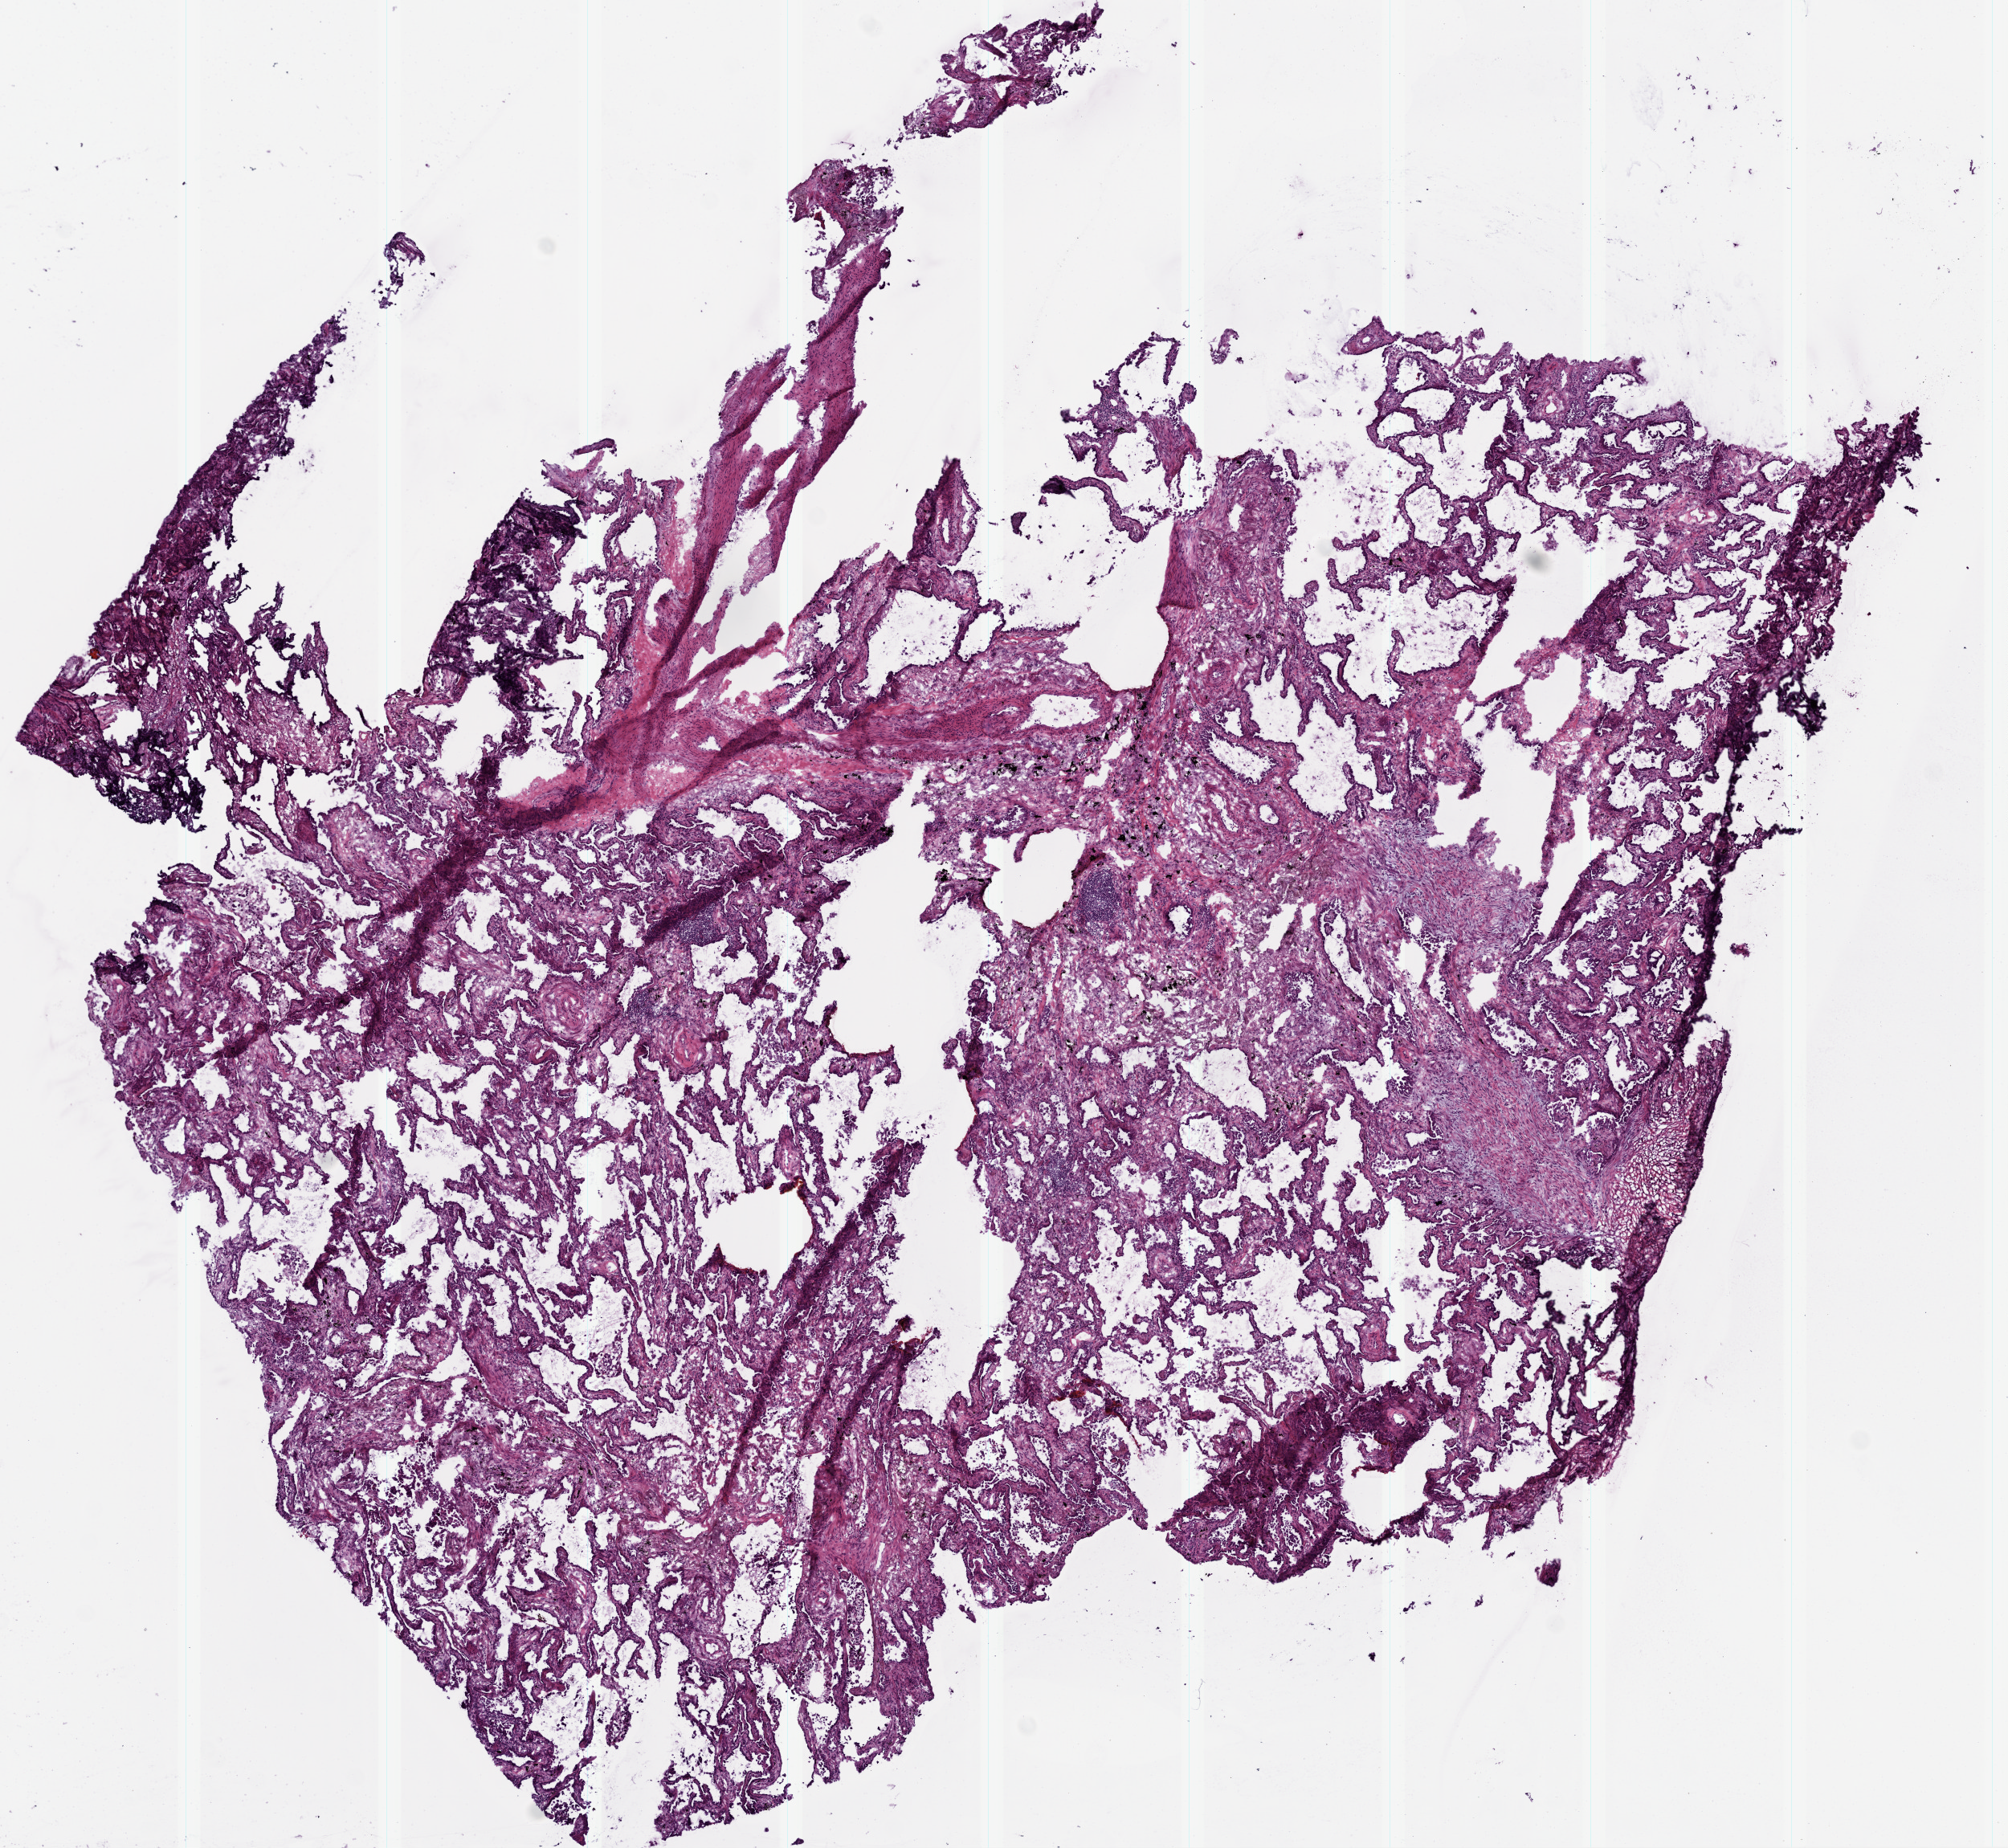
H&E whole-slide image — low-resolution overview of the scanned area, about 10.0 x 9.2 mm (slide scanned at 20x). Frozen section. Sample: primary tumour, lung. Female, age 76 years at initial diagnosis. Composition of this section per pathologist review: tumour cells 80%, tumour nuclei 70%, normal cells 10%, stromal cells 10%, necrosis 0%. Infiltration values recorded for this section: lymphocyte infiltration 10%, monocyte infiltration 0%, neutrophil infiltration 0%.
TNM: T1a N0 MX. Pathologic diagnosis: Bronchiolo-alveolar carcinoma, non-mucinous (upper lobe, lung). AJCC pathologic stage: IA (7th edition).